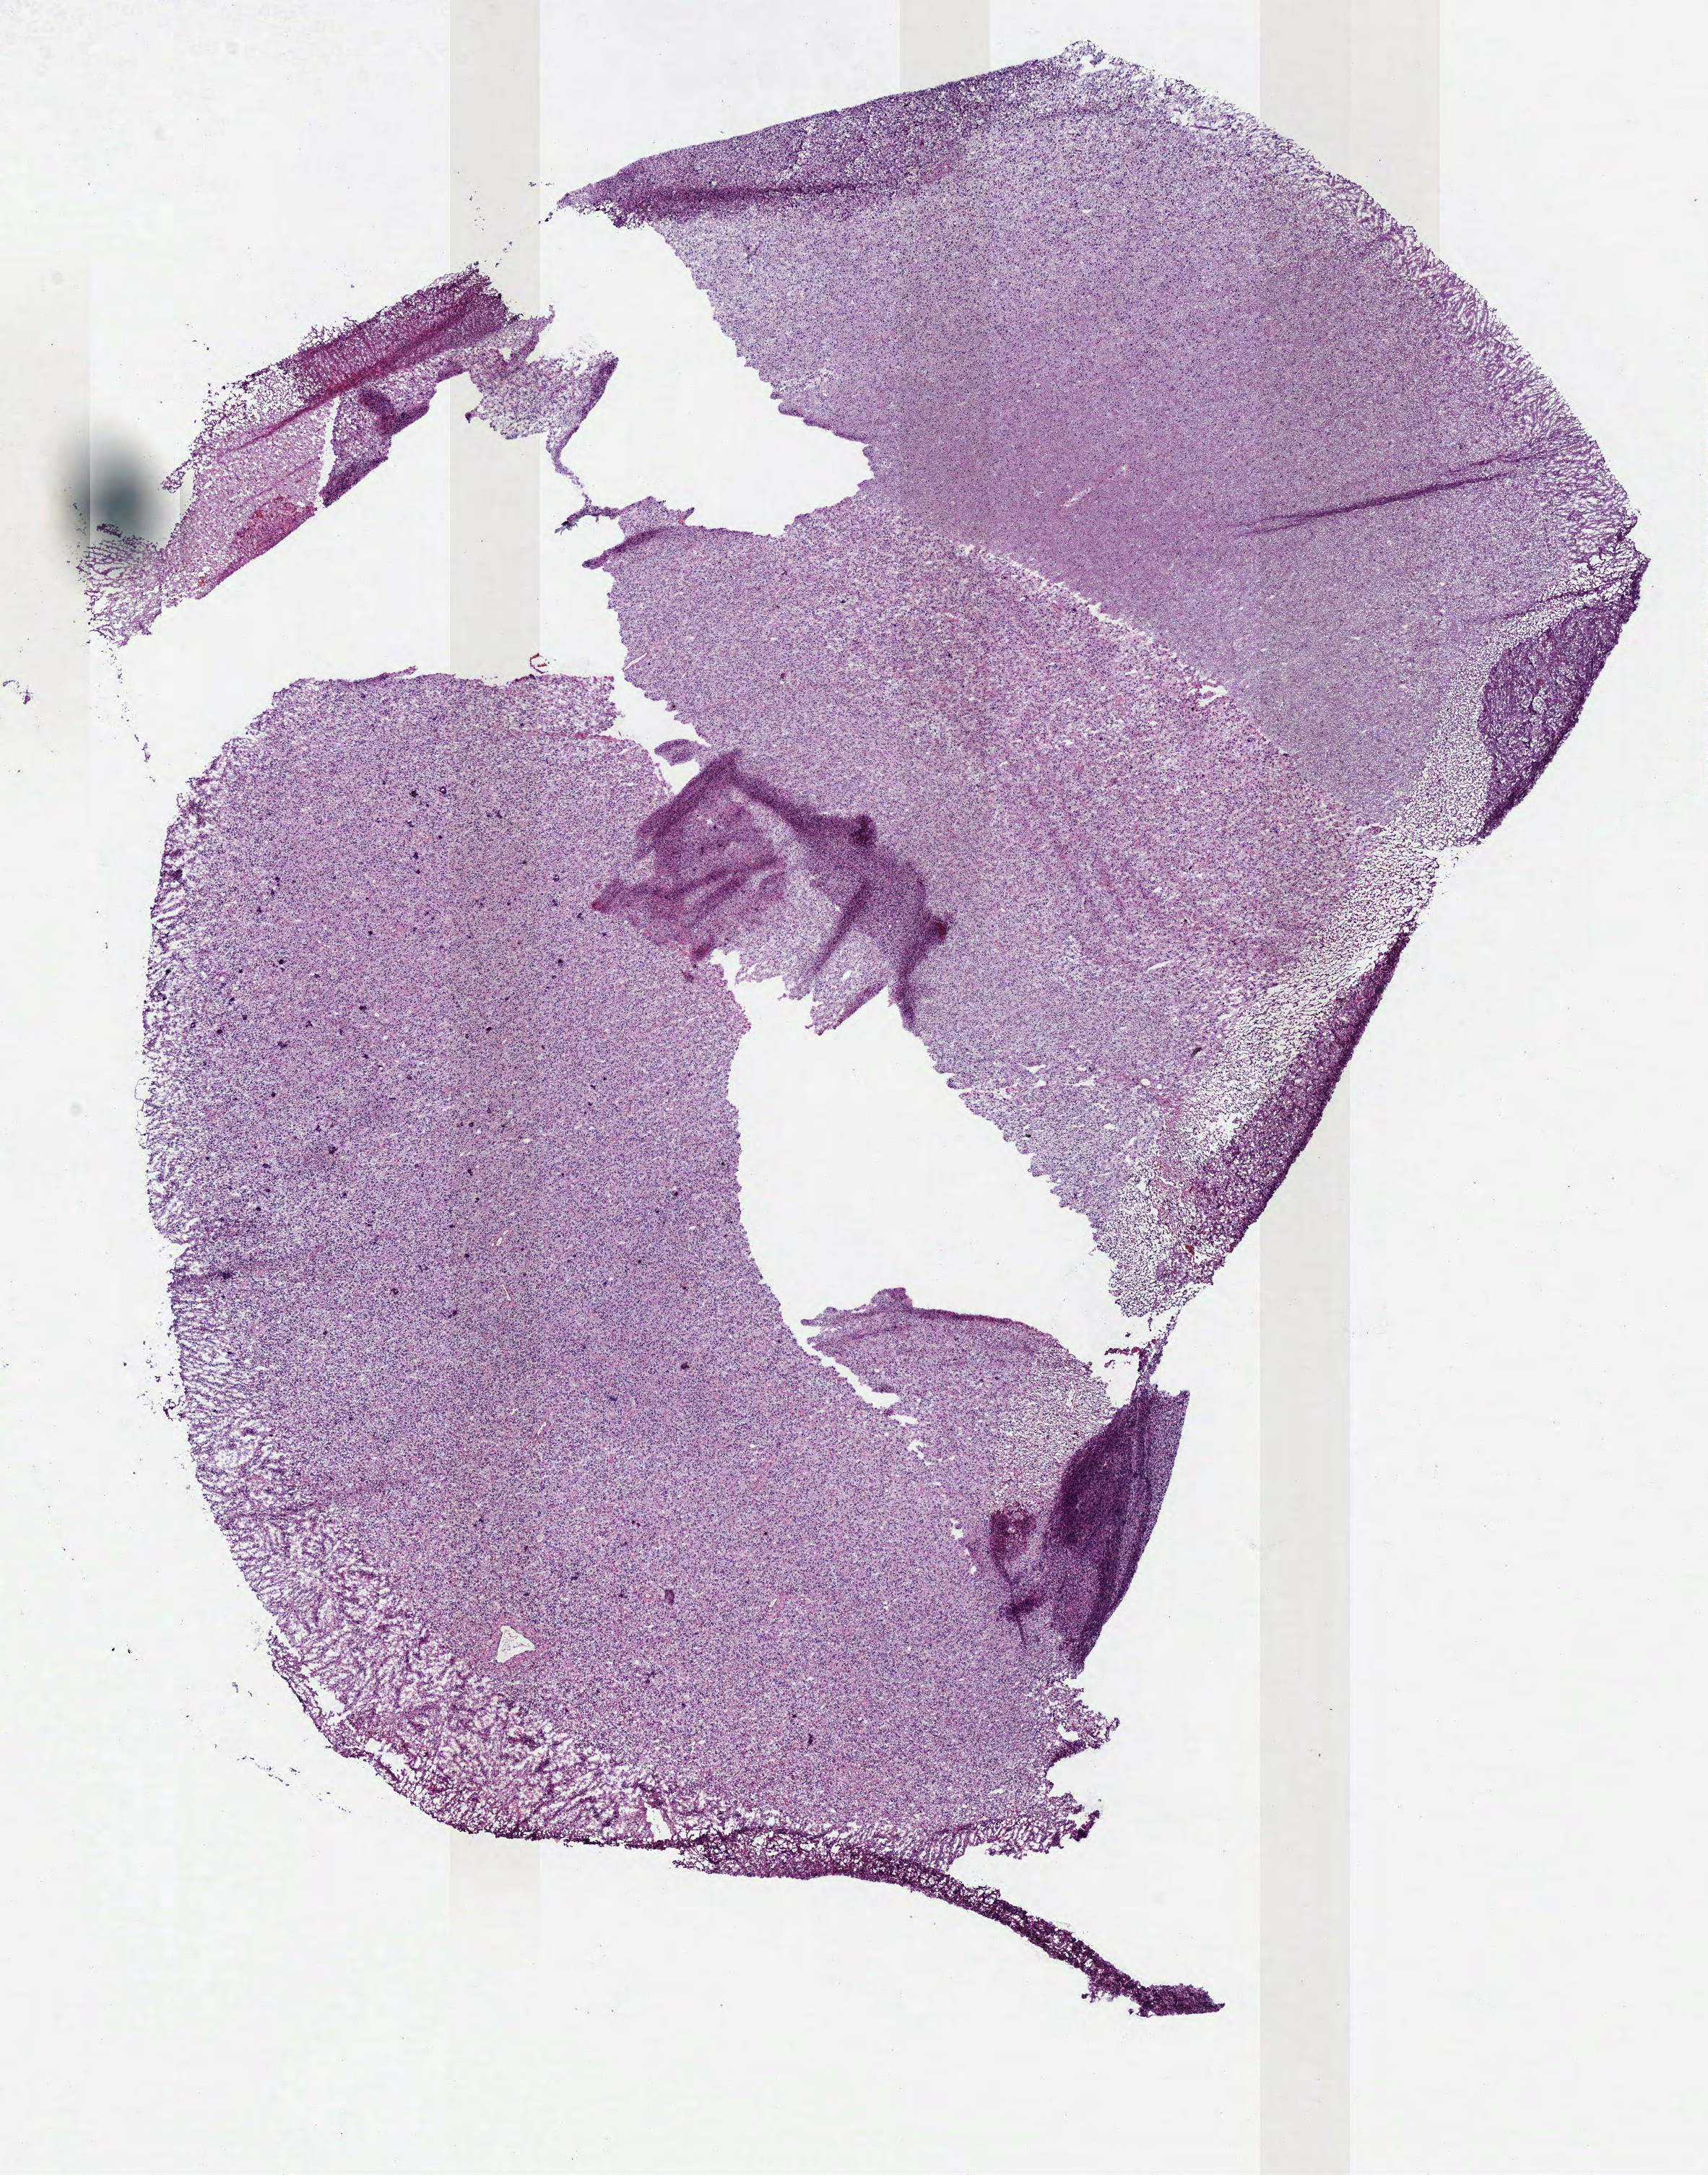
Hematoxylin and eosin (H&E) stained whole-slide image, a low-resolution overview of the entire scanned area, about 9.3 x 11.8 mm (acquisition: 40x scan), frozen section from the top of the tissue portion, primary tumour sample from the brain. Male, age 59 years at initial diagnosis. Histologic grade: G3 (poorly differentiated). Slide review estimates, as recorded: tumour cells 100%, tumour nuclei 80%, normal cells 0%, stromal cells 0%, necrosis 0%.
* pathologic diagnosis: Astrocytoma, anaplastic